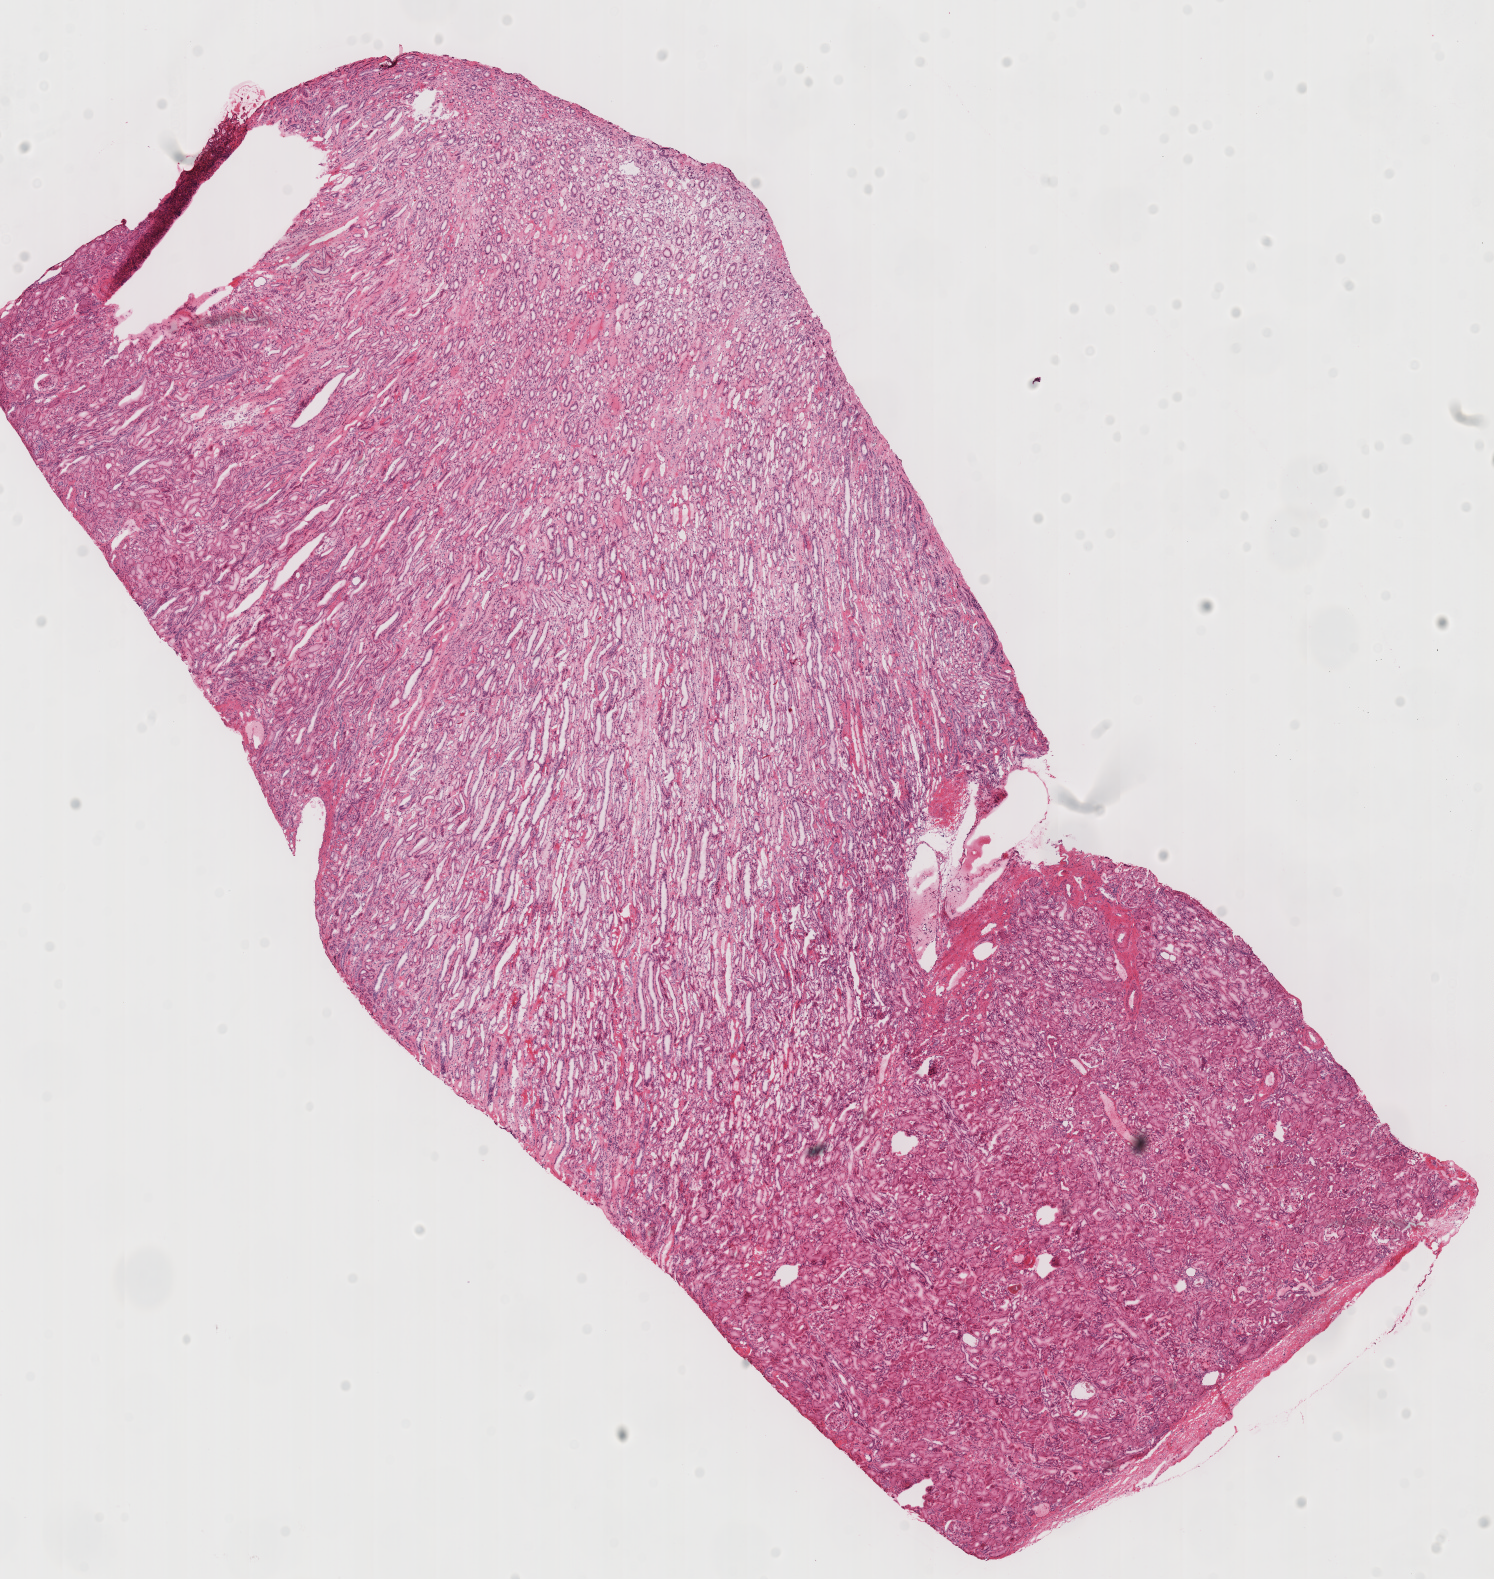
Digitized H&E tissue section (whole slide), whole scanned area (about 11.7 x 12.4 mm) shown as a low-resolution overview. Frozen section from the top of the tissue portion. Sample: solid tissue normal (non-tumour tissue), kidney. Male, age 69 years at initial diagnosis.
This section: solid tissue normal (non-tumour) sample from the same patient. Patient diagnosis: Renal cell carcinoma, chromophobe type.